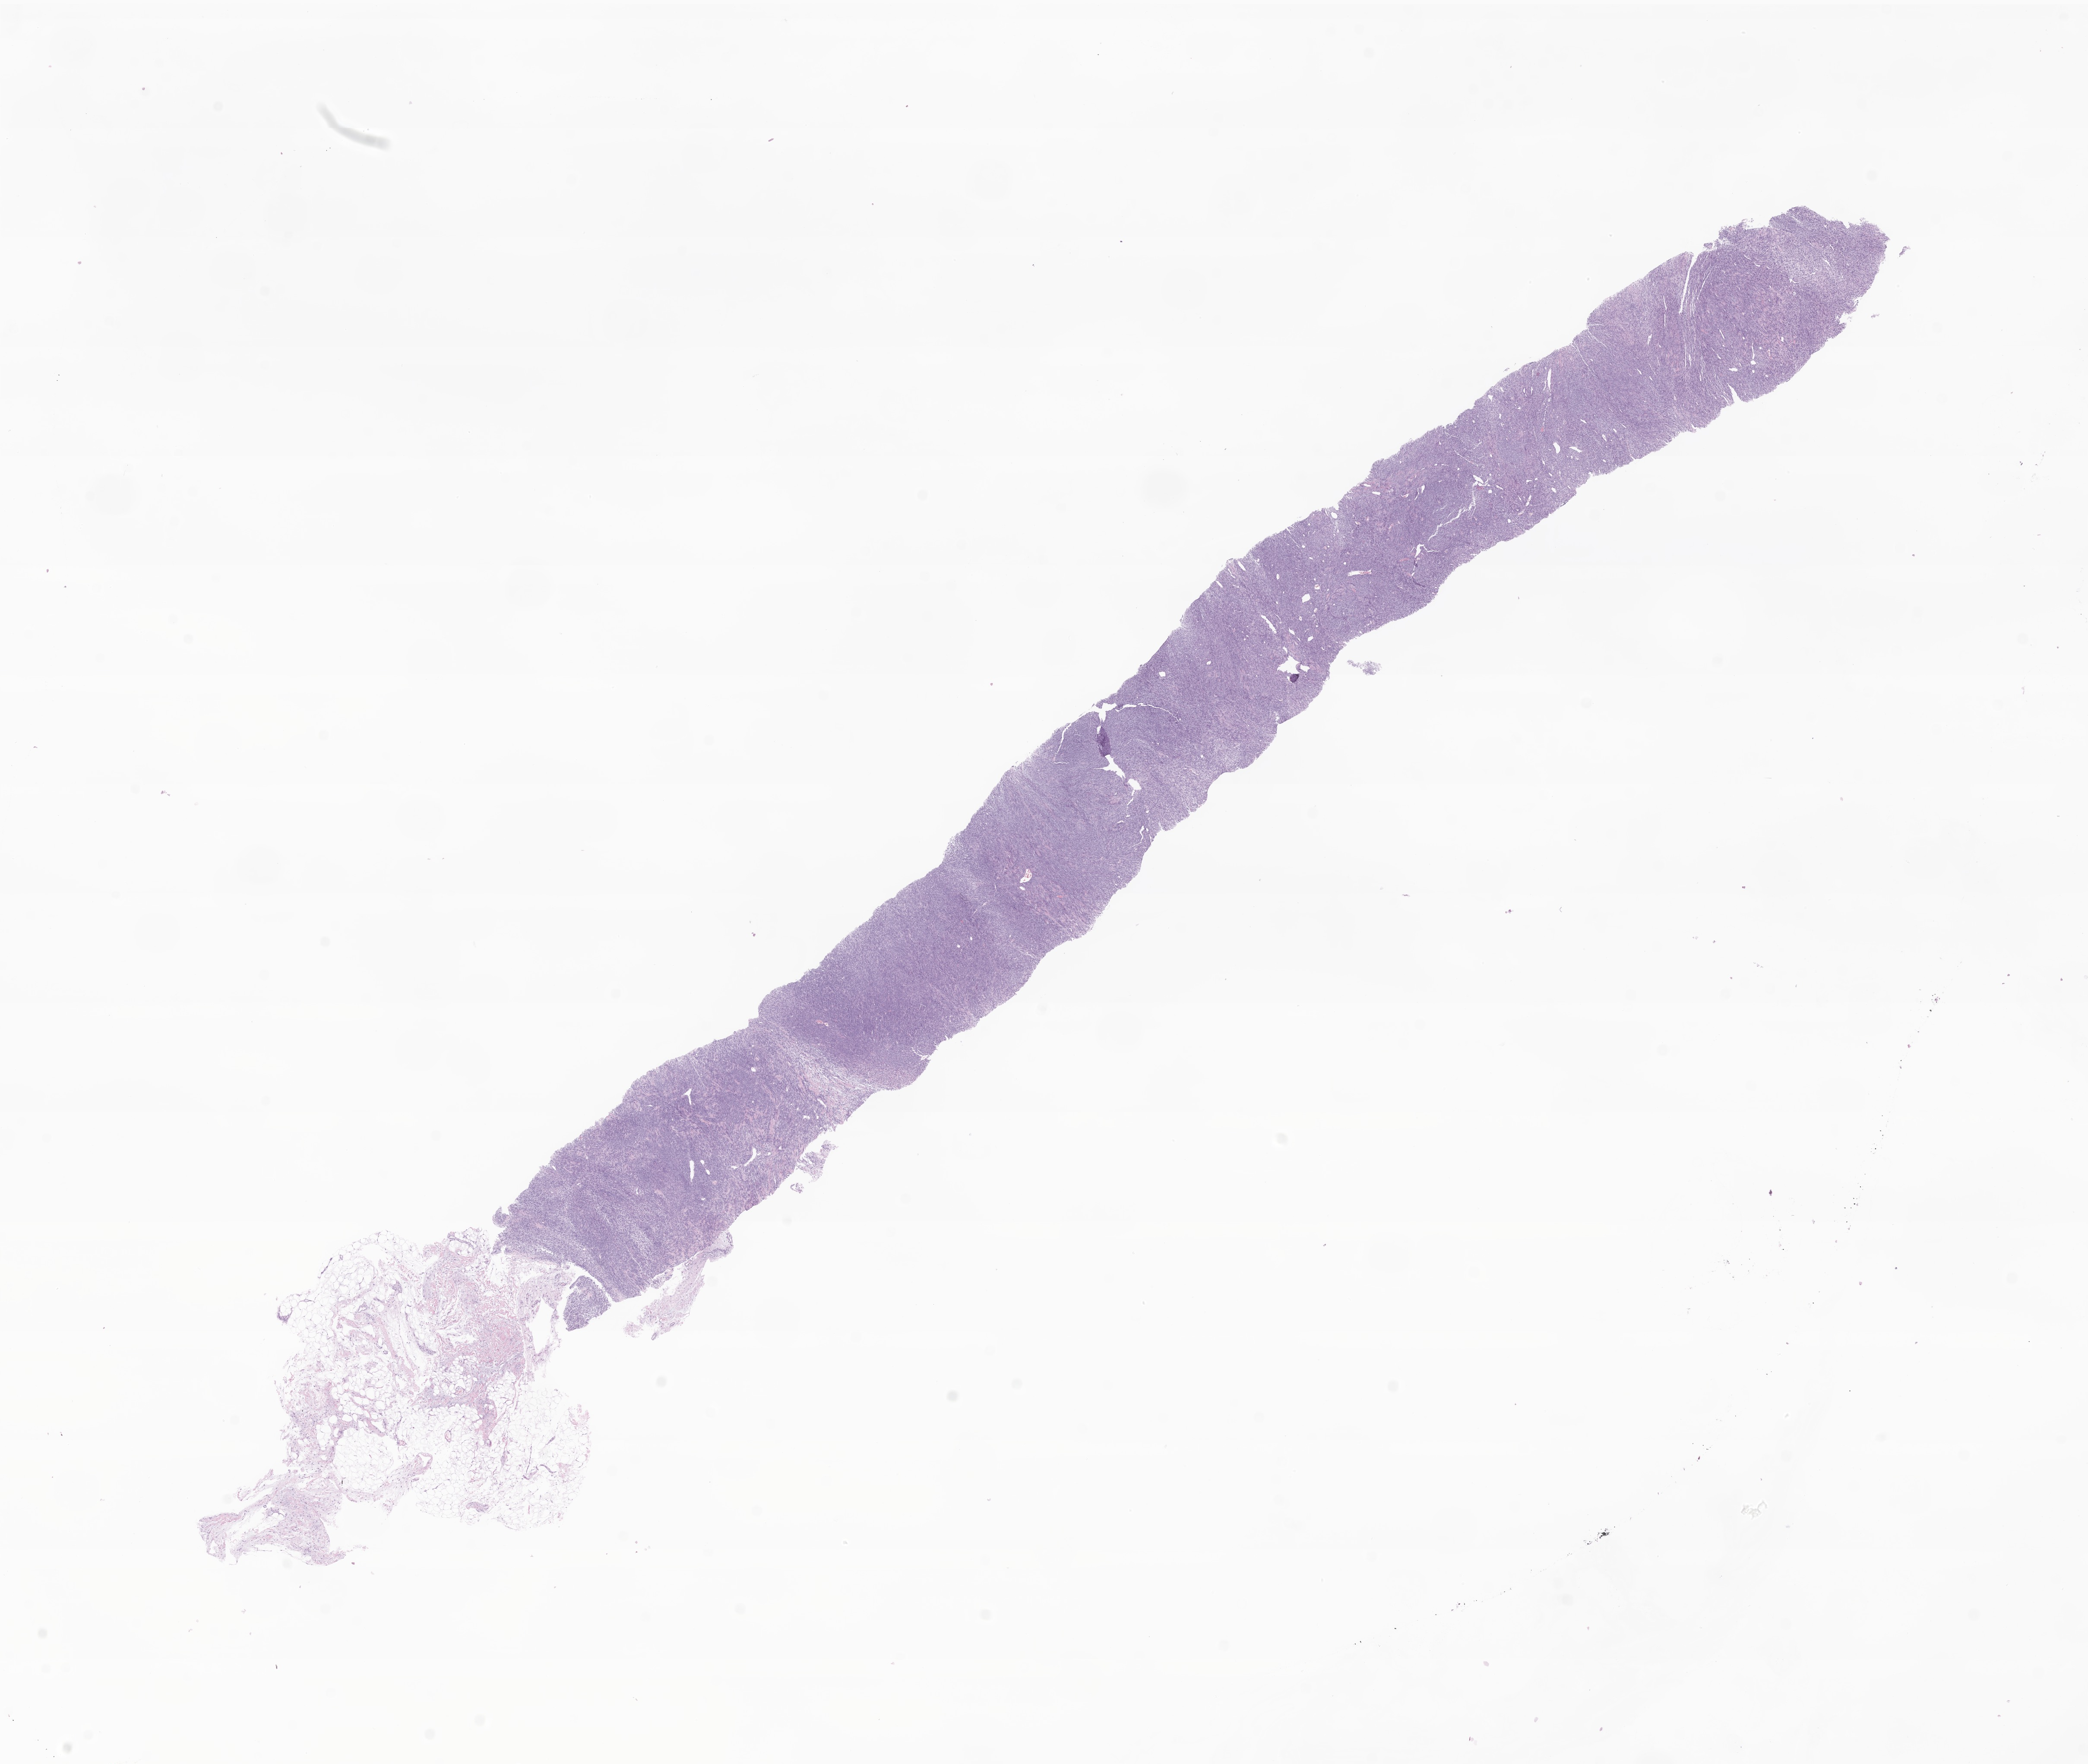
Haematoxylin and eosin whole-slide image of tumor tissue from the thorax, shown as a low-resolution overview of the whole scanned area (about 20.4 x 17.2 mm), FFPE section. Female patient, age 197 months.
Diagnosis: Synovial sarcoma, biphasic.